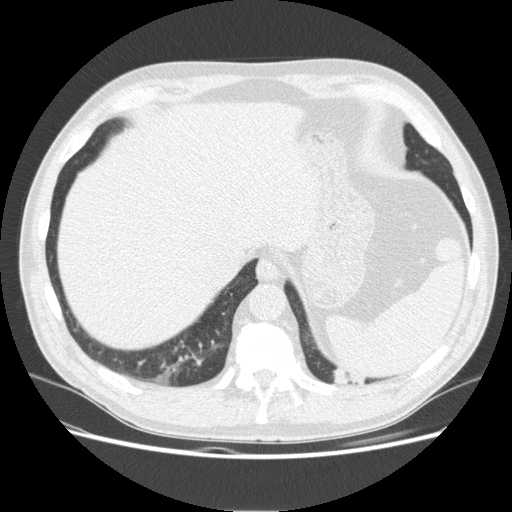
Low-dose screening chest CT, one axial slice. Slice 40 of 165 in the series (ordered by position). Reconstruction kernel STANDARD. Lung window (W 1500 / L -600 HU). 2.5 mm slice thickness. 512 × 512 image matrix.
Structures marked on this image (outlined manually by an expert reader):
- lesion 1 (tumor, upper lobe of left lung): bounding box (x1, y1, x2, y2) in pixels: (333, 369, 366, 384)